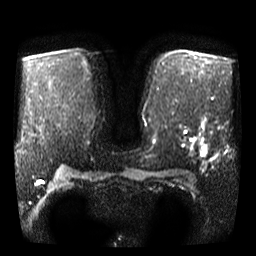
Breast MRI, one axial slice; diffusion-weighted series; image 2 of 4 stored at this slice position (different b-values; order by instance number); 3 T; 256 × 256 image matrix. Female patient.
Annotated regions visible in this slice (expert manual segmentation):
- tumour on diffusion-weighted imaging: box from (x=201, y=146) to (x=207, y=156) px